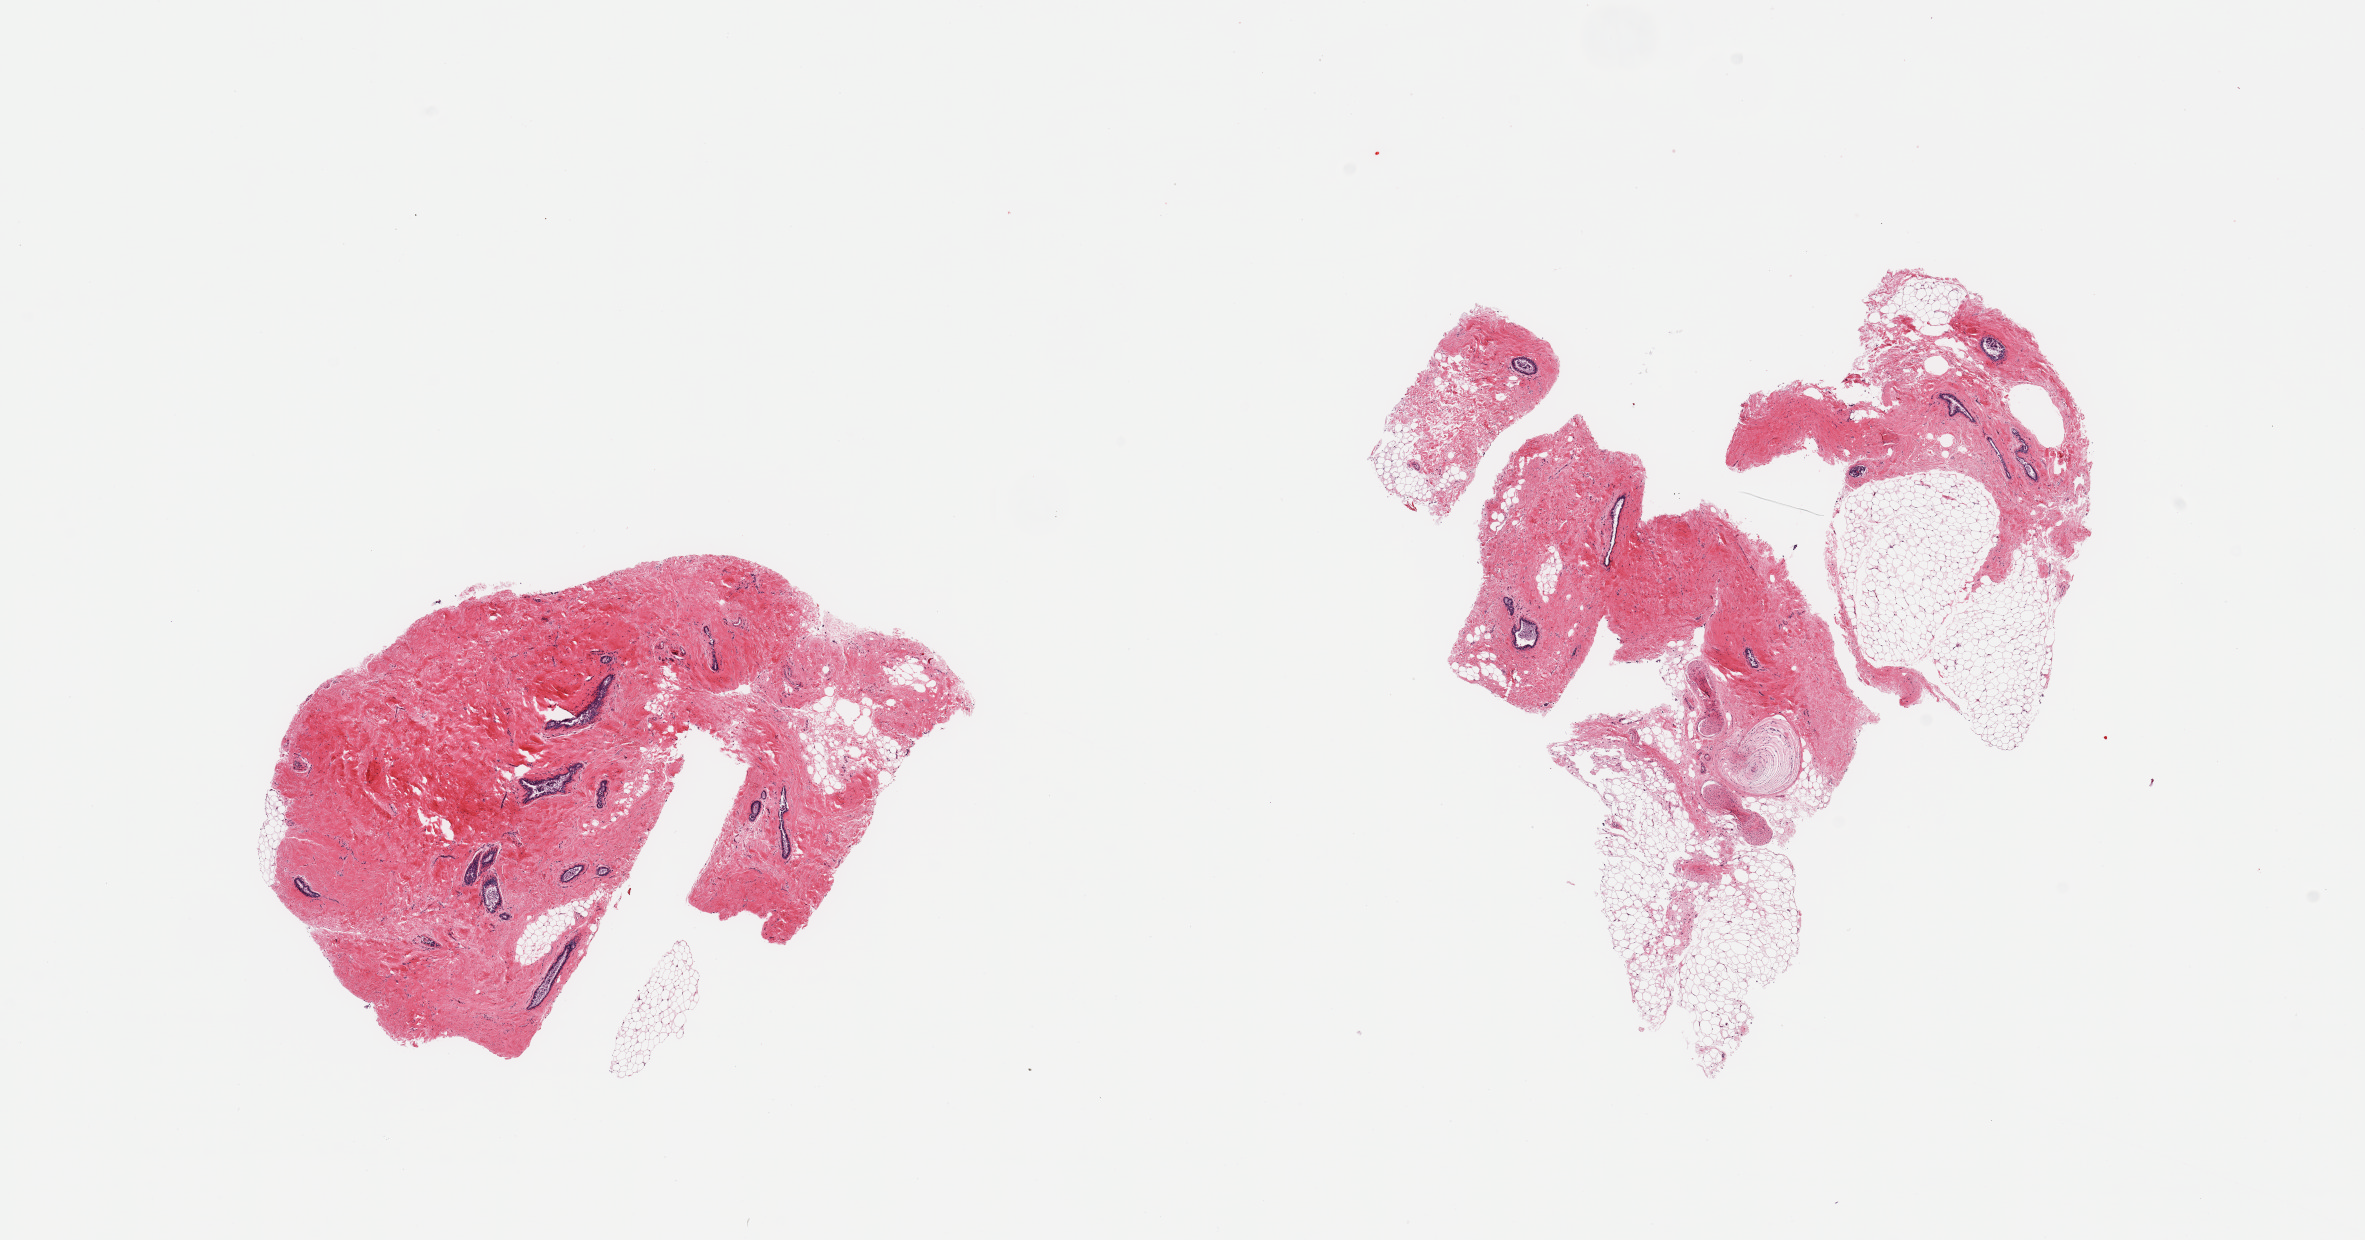
Hematoxylin and eosin (H&E) whole-slide image, low-resolution overview of the scanned area, about 18.7 x 9.8 mm (acquisition: 20x scan). PAXgene-fixed, paraffin-embedded tissue. Target tissue: breast. Donor tissue sample.
- reviewer comment on this tissue sample: 2 pieces, gynecomastoid stromal and ductal hyperplasia